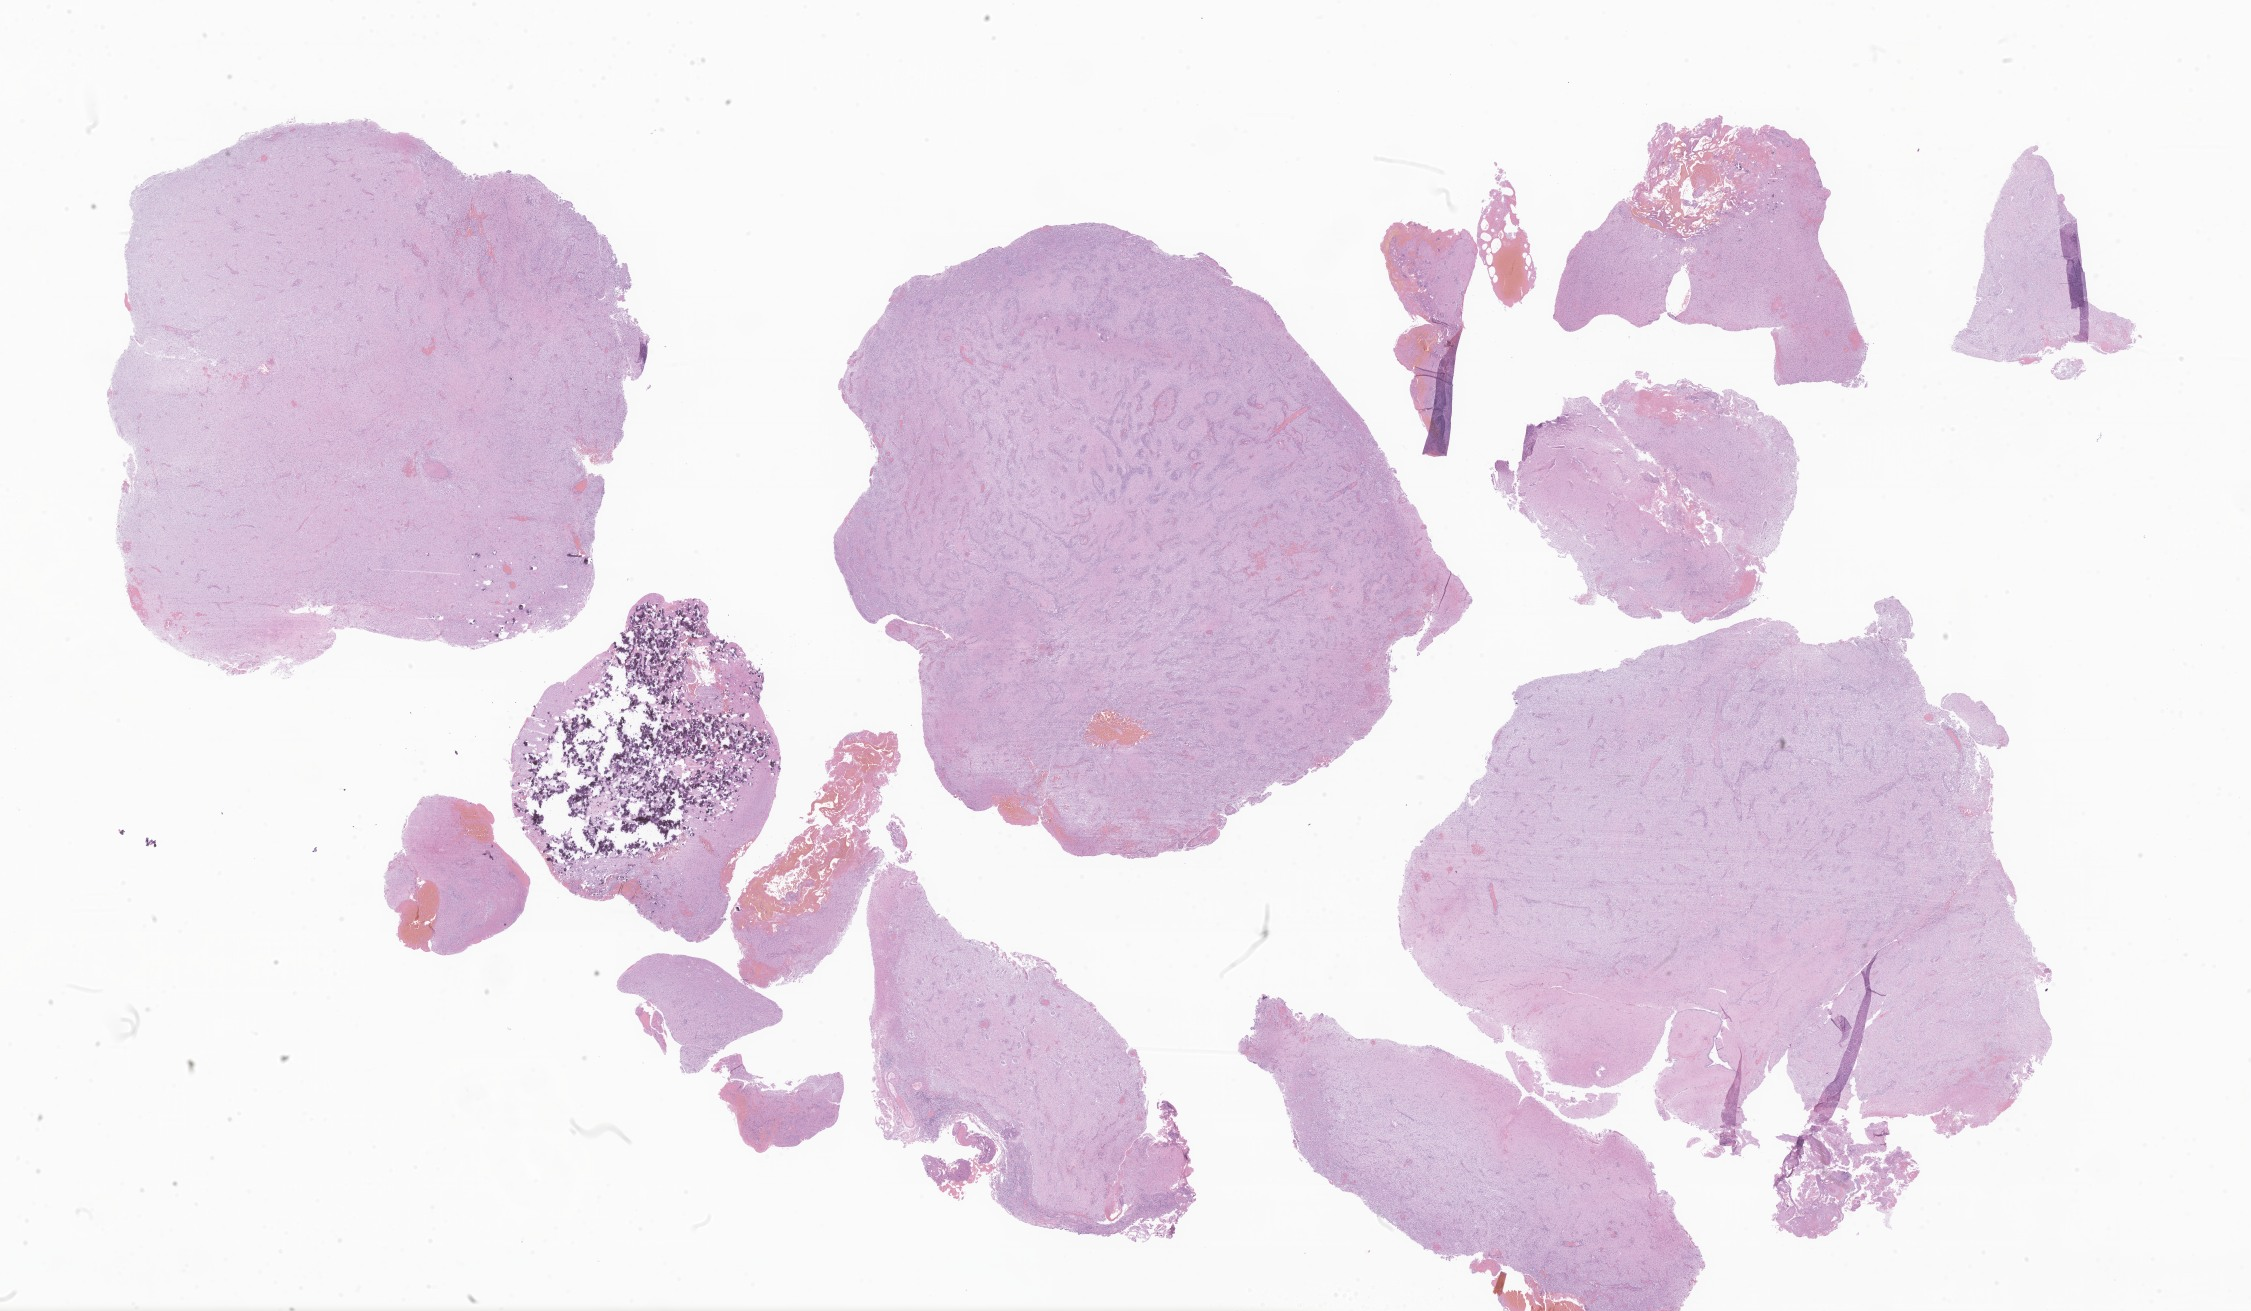
Whole-slide image, hematoxylin and eosin (H&E) stain of tumor tissue from the brain — a low-resolution overview of the entire scanned area, about 38.0 x 22.1 mm, formalin-fixed, paraffin-embedded (FFPE) tissue. Patient: female, age 162 months (13 years 6 months).
Recorded diagnosis: Pilocytic astrocytoma.